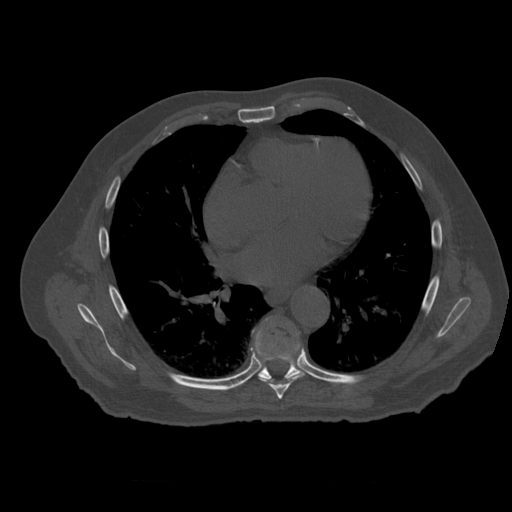
CT including the spine, one axial slice; position 352 of 399 along the scan axis; 120 kVp; bone window (W 1800 / L 400 HU); 1.25 mm slice thickness; 512 × 512 image matrix. Patient age 73 years. From the clinical record (not read from this slice): primary cancer: prostate; vertebrae with lytic lesions (as recorded): L2.
Structures marked on this image (semi-automatic segmentation, software-assisted and operator-edited):
- T7 vertebra: bounding box [x1, y1, x2, y2] px = [255, 349, 305, 400]
- T8 vertebra: [251, 332, 302, 381]